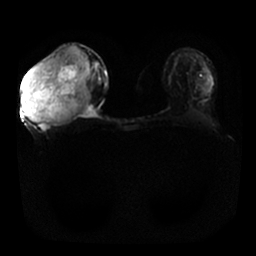
Breast MRI, one axial slice. Position 10 of 25 along the scan axis. Diffusion-weighted series; image 2 of 4 stored at this slice position (different b-values; order by instance number). 1.5 T. 4 mm slice thickness. 256 × 256 image matrix, field of view 340 × 340 mm. Female patient.
Annotated regions visible in this slice (manually delineated by an expert):
- tumour on diffusion-weighted imaging: bounding box <22,46,89,124> (left, top, right, bottom; pixels)